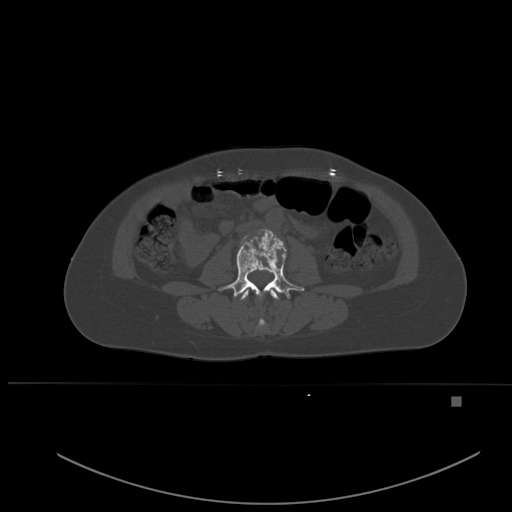
CT including the spine, one axial slice; position 196 of 651 along the scan axis; bone window (W 1800 / L 400 HU); 512 × 512 image matrix. Female patient, age 49 years. Case-level facts recorded for this patient, not image findings: primary cancer: breast; vertebrae with lytic lesions (as recorded): L3, T12, L4.
Structures marked on this image (semi-automatically segmented with operator editing):
- L2 vertebra: bounding box (x1, y1, x2, y2) in pixels: (240, 290, 279, 326)
- L3 vertebra: (219, 231, 304, 299)